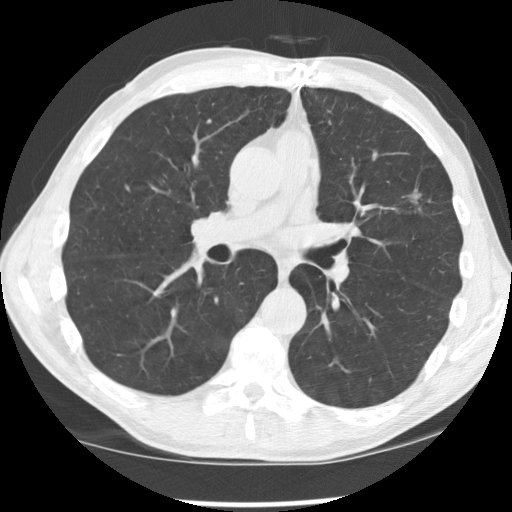
Low-dose screening chest CT, one axial slice. Slice 95 of 170 in the series (ordered by position). Reconstruction kernel STANDARD. Lung window (W 1500 / L -600 HU). 512 × 512 image matrix, field of view 340 × 340 mm.
Outlined on this slice (outlined manually by an expert reader):
- lesion 1 (tumor, upper lobe of left lung): bounding box [x1, y1, x2, y2] px = [410, 189, 421, 203]